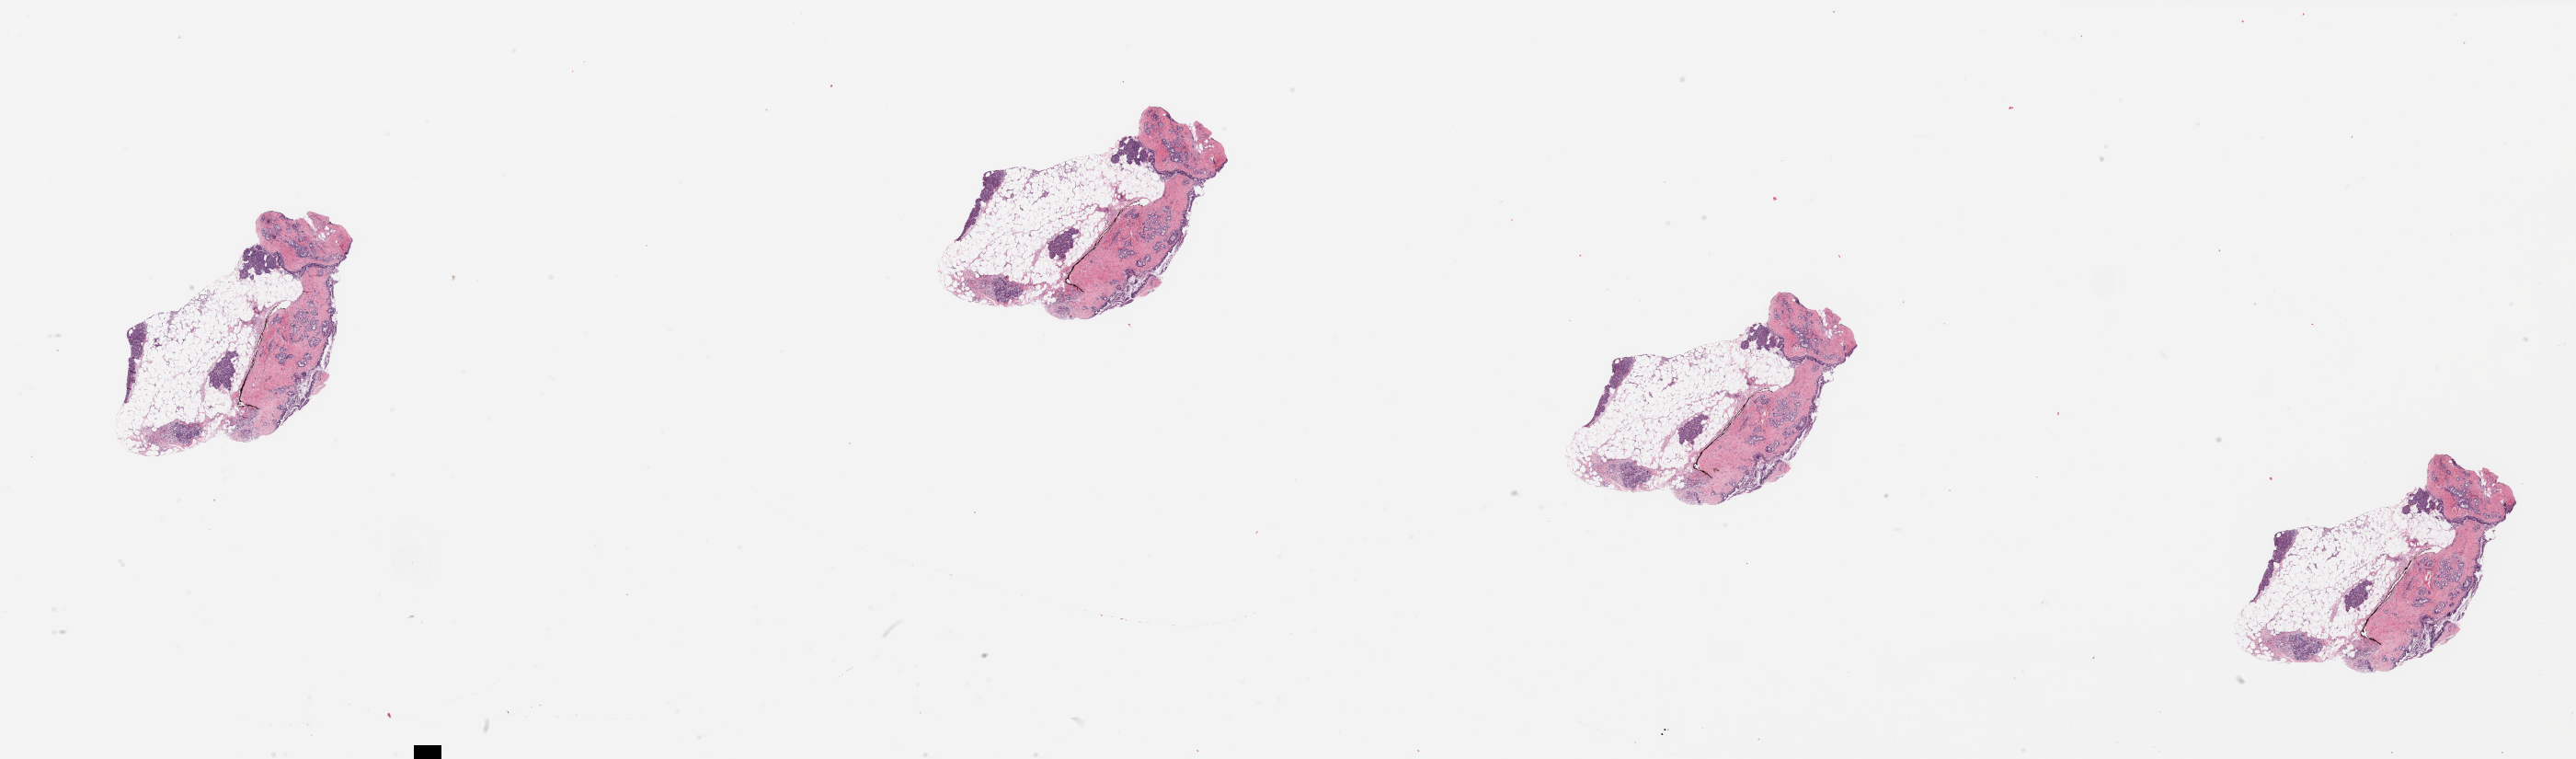
Digitized H&E-stained tissue section (whole slide), low-resolution overview of the scanned area, about 44.3 x 13.0 mm (acquisition: 20x scan); normal (non-tumour) tissue sample, pancreas. 67-year-old female patient.
- this section: normal (non-tumour) tissue from the same patient
- patient diagnosis: Infiltrating duct carcinoma, NOS